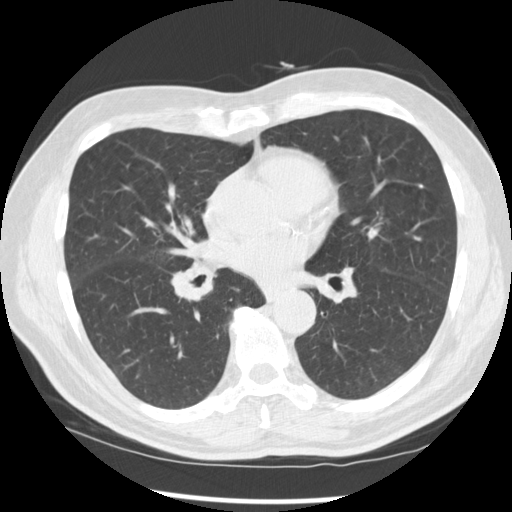
Chest CT (low-dose screening protocol), one axial image, first (baseline) screen, lung window (W 1500 / L -600 HU), 512 × 512 image matrix. Male participant, aged 67 years at enrolment.
• Lesion marked by an expert reader, box from (x=155, y=245) to (x=227, y=313) px.
• Screening reader's record for this exam (one nodule recorded; not confirmed to be the boxed lesion): non-calcified nodule or mass ≥4 mm, left lower lobe, 15 × 15 mm, spiculated (stellate) margins, soft tissue attenuation.
• Note: the box lies in the patient's right hemithorax on this image, whereas the reader's record names the left lung; they may be different findings.